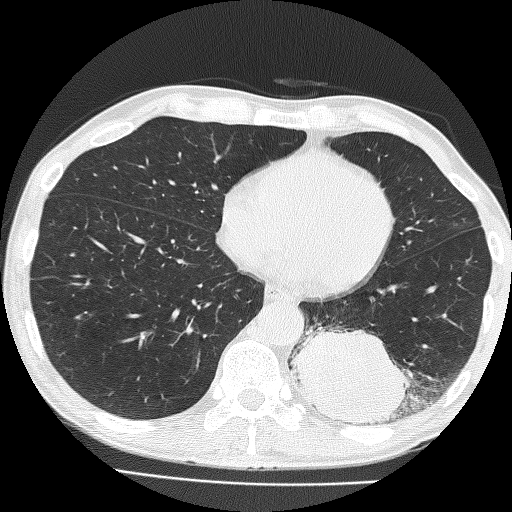
Low-dose screening chest CT, one axial slice. Slice 60 of 160 in the series (ordered by position). Reconstruction kernel FC51. 120 kVp. Lung window (W 1500 / L -600 HU). 2 mm slice thickness. 512 × 512 image matrix.
Outlined on this slice (expert manual segmentation):
- lesion 1 (tumor, lower lobe of left lung): bounding box <293,328,411,425> (left, top, right, bottom; pixels)